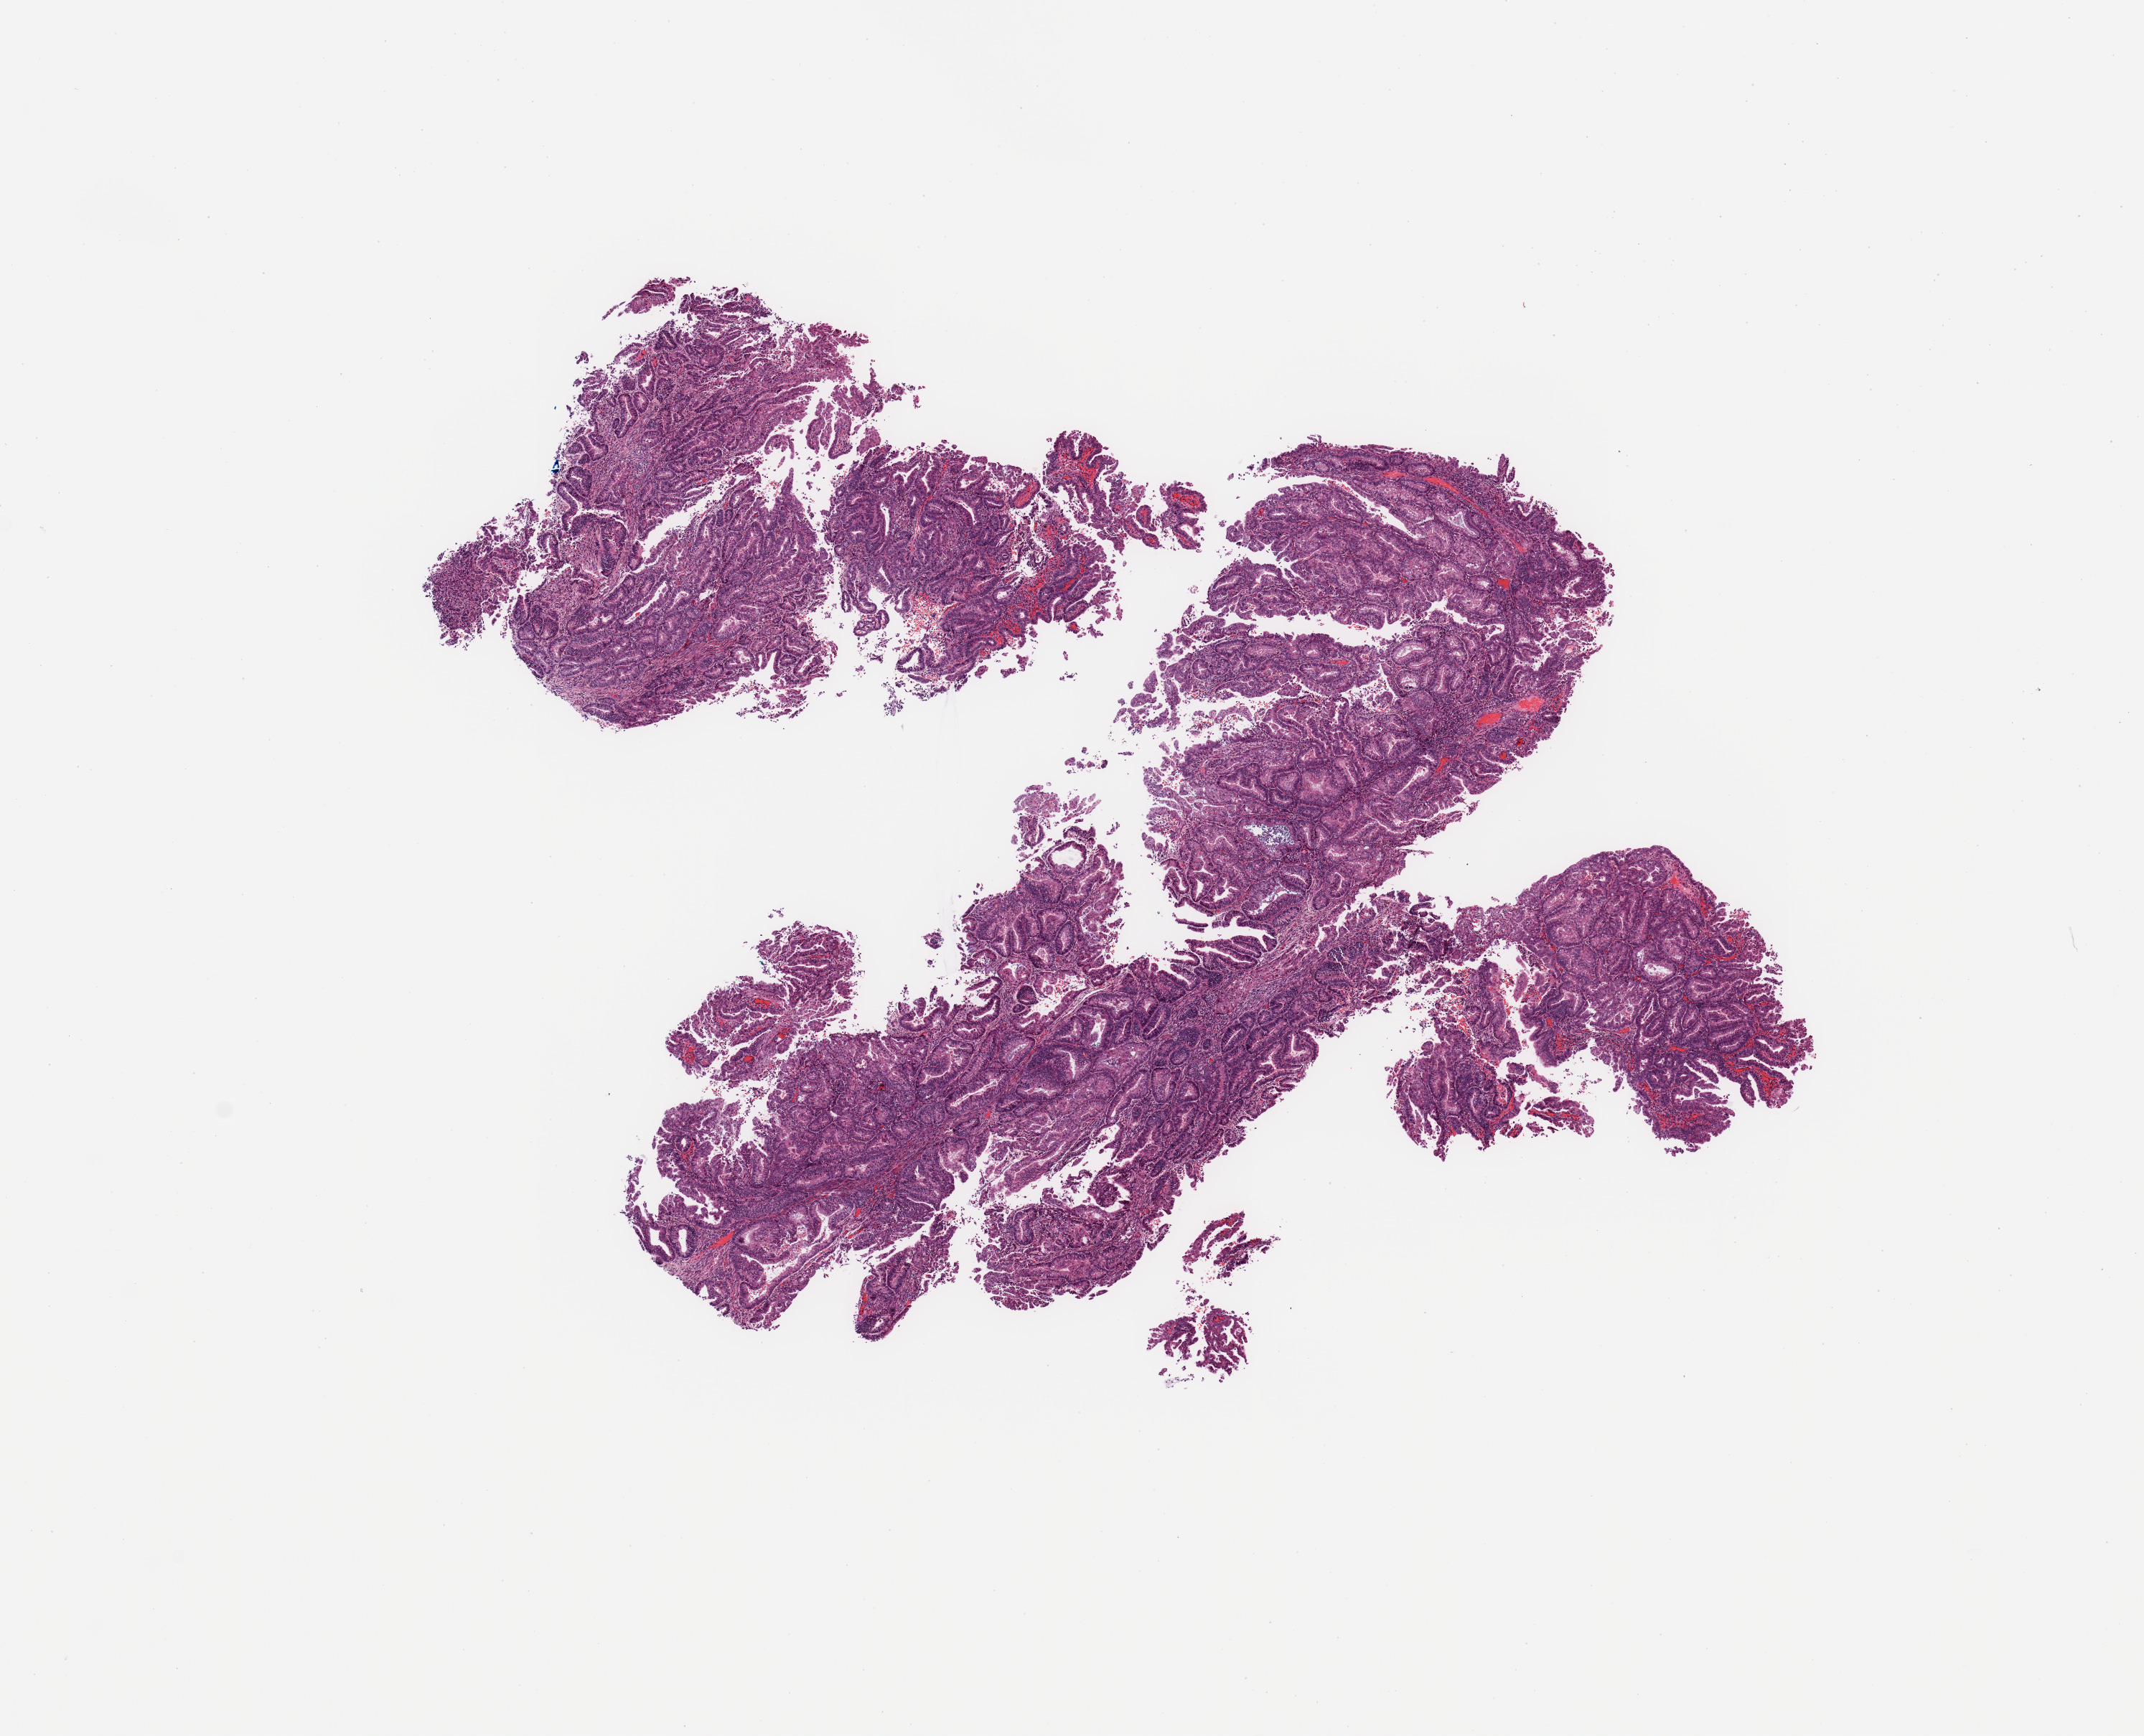
Whole-slide histology image, H&E-stained — low-resolution overview of the scanned area, about 11.8 x 9.6 mm (from a 20x scan). Tumour tissue sample, sampled site: uterus. Patient: female, age 68 years. Histologic grade: G1 (well differentiated). Composition of this section per pathologist review: tumour nuclei 90%, necrosis 1%.
Histologic diagnosis: Endometrioid adenocarcinoma, NOS. AJCC pathologic stage: I.